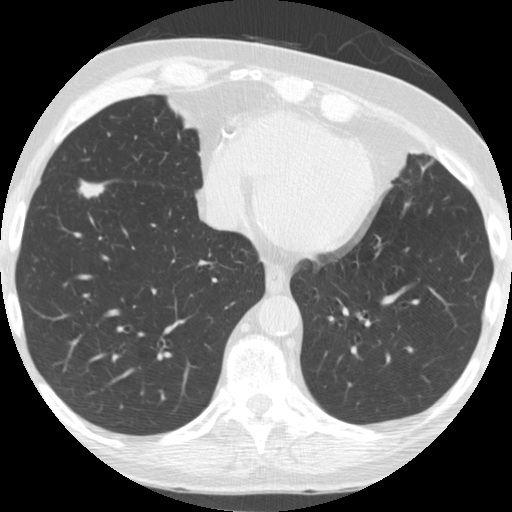
Low-dose screening chest CT, one axial slice. Position 69 of 182 along the scan axis. Reconstruction kernel STANDARD. 120 kVp. Lung window (W 1500 / L -600 HU). 512 × 512 image matrix, field of view 320 × 320 mm.
Outlined on this slice (manually delineated by an expert):
- lesion 1 (tumor, lower lobe of right lung): box from (x=78, y=180) to (x=107, y=199) px